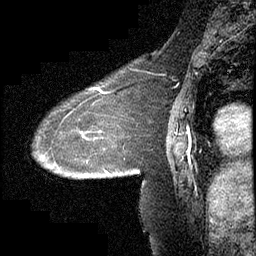
Breast MRI (dynamic contrast-enhanced), one sagittal slice; slice 142 of 232 in the series (ordered by position); dynamic contrast-enhanced study with each time point stored as its own series, time point 2 of 4 at this slice position (early post-contrast, ordered by acquisition time); 1.5 T; TE 4.2 ms, TR 6.7 ms; 3 mm slice thickness; 256 × 256 image matrix. Female patient, age 63 years. From the clinical record (not read from this slice): setting: breast cancer imaged before/during neoadjuvant chemotherapy; receptor status: triple-negative.
Structures marked on this image (semi-automatic segmentation, software-assisted and operator-edited):
- analysis volume of interest (the breast-tissue region the enhancement analysis was run in; not a lesion): bounding box [x1, y1, x2, y2] px = [34, 90, 140, 180]
- tumour enhancement mask (voxels above the 70 % enhancement threshold inside the analysis volume of interest): [99, 90, 110, 172]